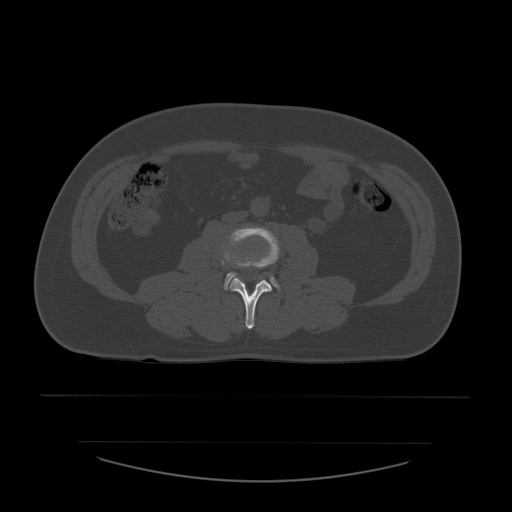
CT including the spine, one axial slice. Slice 164 of 532 in the series (ordered by position). Bone window (W 1800 / L 400 HU). 512 × 512 image matrix, field of view 441 × 441 mm. Patient age 44 years. Case-level facts recorded for this patient, not image findings: primary cancer: soft tissue sarcoma.
Structures marked on this image (semi-automatic segmentation, software-assisted and operator-edited):
- L3 vertebra: box from (x=221, y=227) to (x=280, y=329) px
- L4 vertebra: (x=224, y=272)–(x=280, y=290)